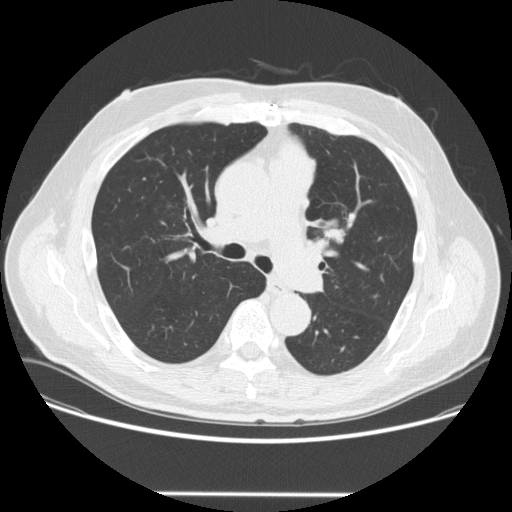
Low-dose screening chest CT, one axial slice; 120 kVp; lung window (W 1500 / L -600 HU); 2.5 mm slice thickness; 512 × 512 image matrix, field of view 400 × 400 mm.
Outlined on this slice (outlined manually by an expert reader):
- lesion 1 (tumor, upper lobe of left lung): bounding box <327,228,343,241> (left, top, right, bottom; pixels)